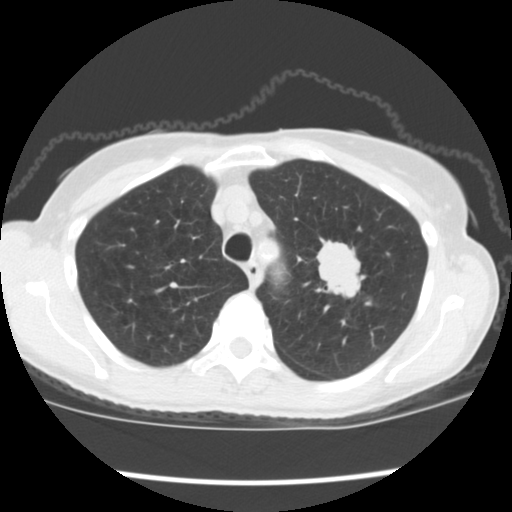
Chest CT (low-dose screening protocol), one axial image. Baseline screening round. Lung window (W 1500 / L -600 HU). Slice 35 of 176 in the series. 512 × 512 image matrix, field of view 318 × 318 mm. Female, age 67 years at enrolment. Former smoker at enrolment.
- Expert reader's lesion annotation, bounding box [x1, y1, x2, y2] px = [305, 235, 378, 311].
- Screening reader's record for this exam (one nodule recorded; not confirmed to be the boxed lesion): non-calcified nodule or mass ≥4 mm, left upper lobe, 34 × 32 mm, spiculated (stellate) margins, soft tissue attenuation, pre-existing on the prior screen: no.
- Lung cancer was diagnosed 17 days after this screen: small cell carcinoma, NOS, left upper lobe, stage IIIA (AJCC 6th edition), 40 mm at pathology.